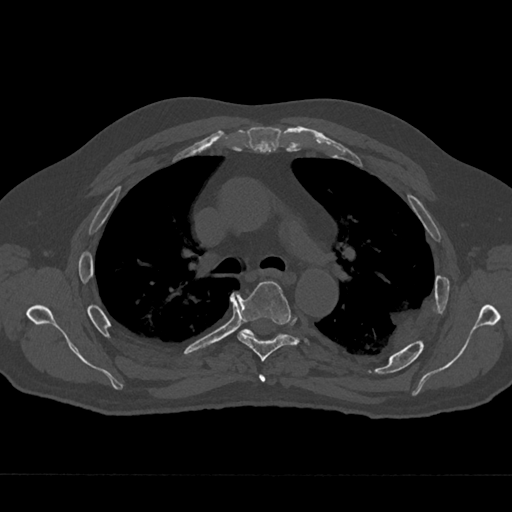
CT including the spine, one axial slice; 120 kVp; bone window (W 1800 / L 400 HU); 0.5 mm slice thickness; 512 × 512 image matrix. Patient: male, 75 years. Case-level facts recorded for this patient, not image findings: primary cancer: renal; vertebrae with lytic lesions (as recorded): T4.
Annotated regions visible in this slice (semi-automatic segmentation, software-assisted and operator-edited):
- T4 vertebra: bounding box <259,374,266,382> (left, top, right, bottom; pixels)
- T5 vertebra: <236,281,310,361>
- T6 vertebra: <241,328,254,336>